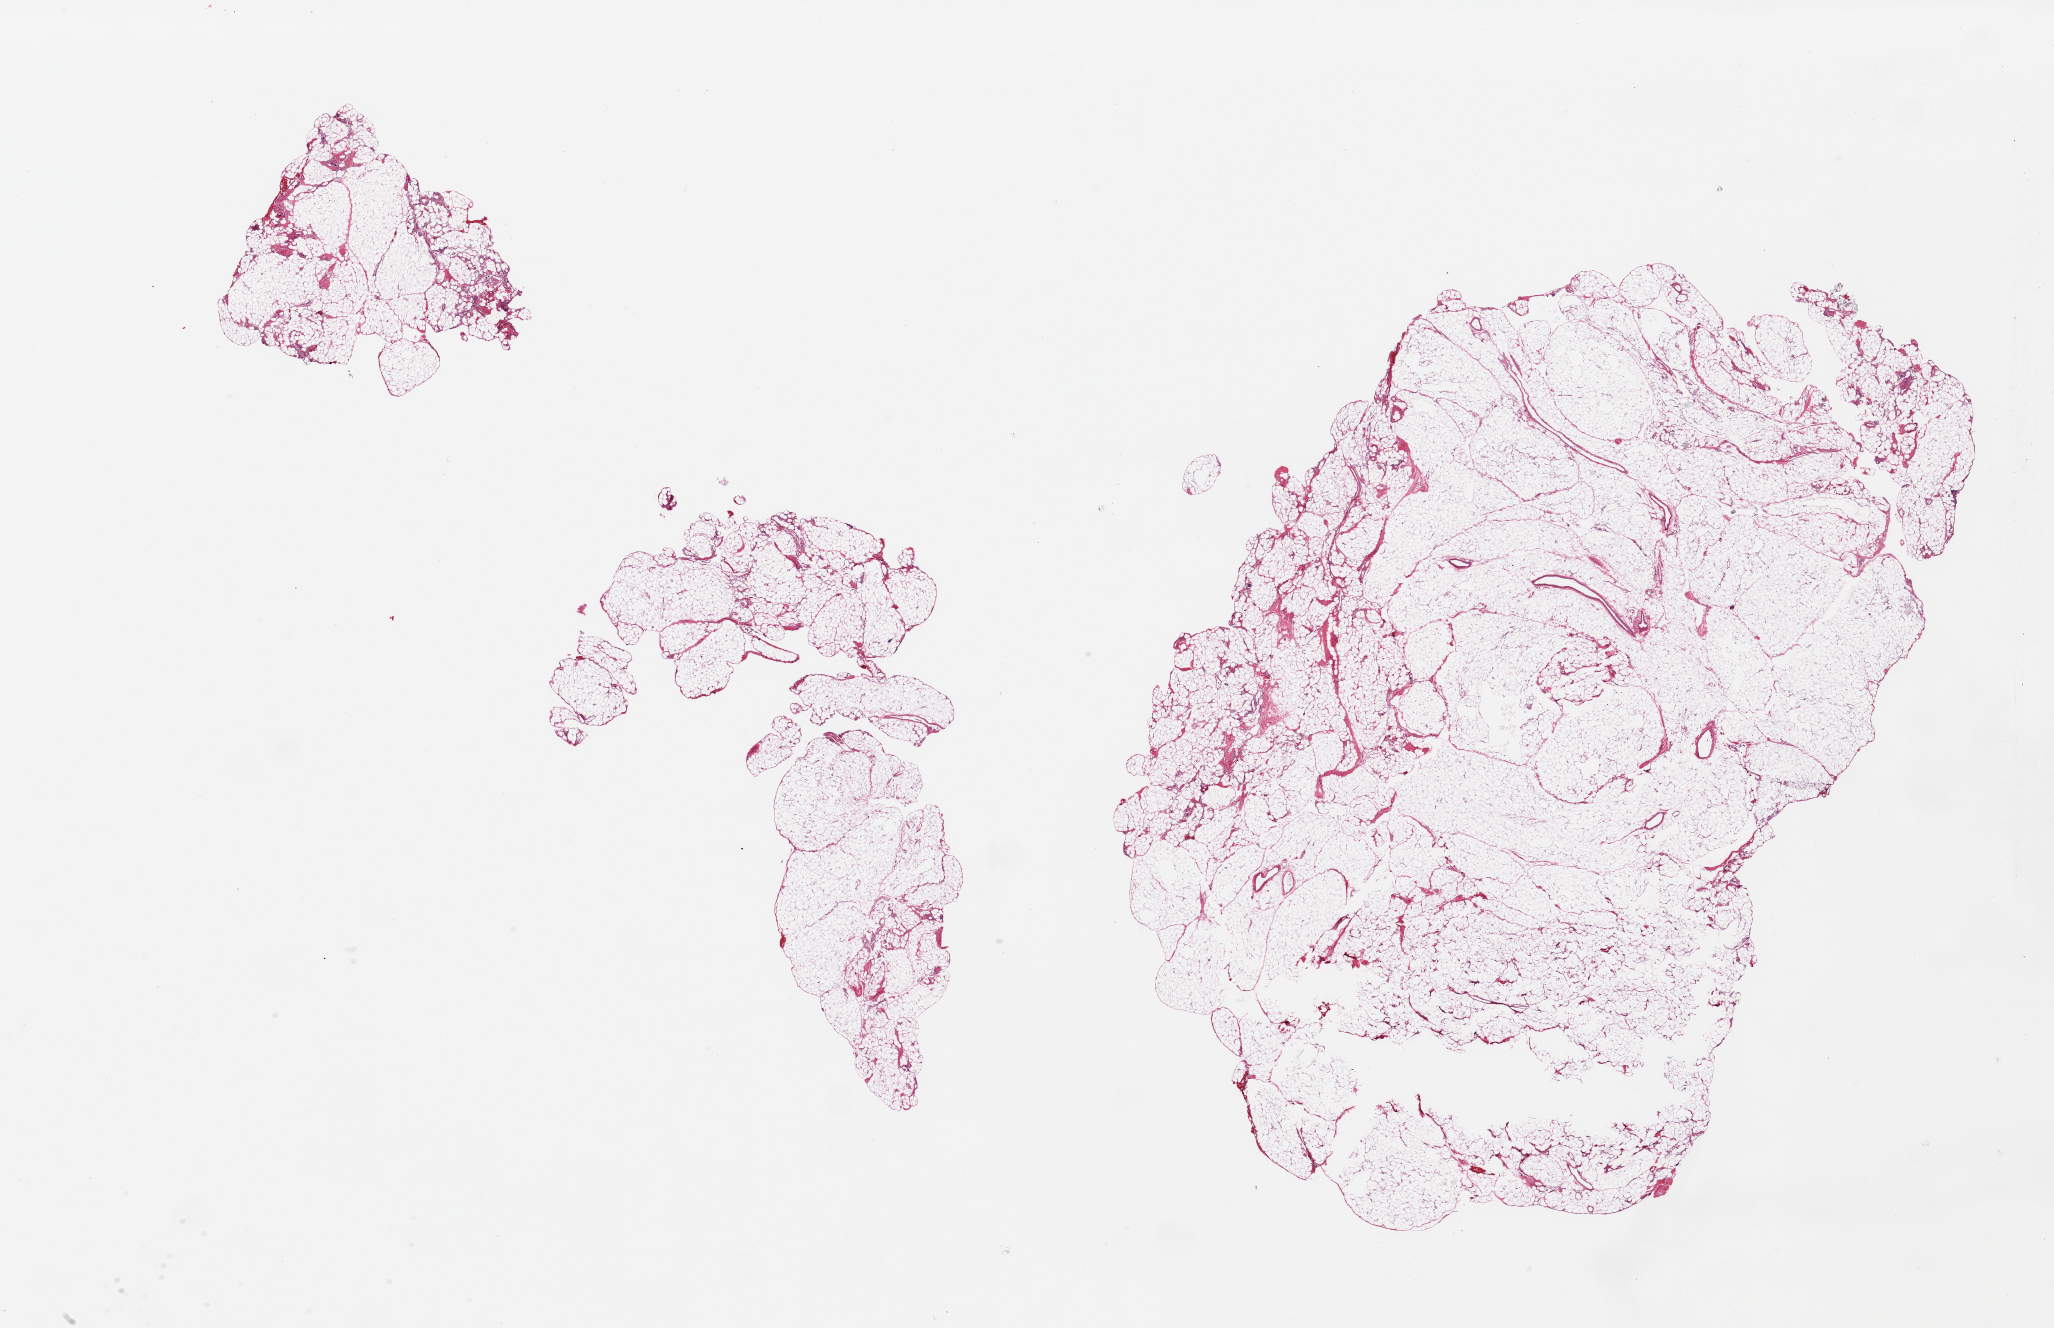
Digitized hematoxylin and eosin (H&E)-stained section, brightfield, low-resolution overview of the scanned area, about 32.5 x 21.0 mm; PAXgene-fixed paraffin-embedded (PFPE) section; section of omentum (target tissue); tissue donor sample.
Reviewer comment on this tissue sample: 3 pieces; lobulated mature adipose tissue.